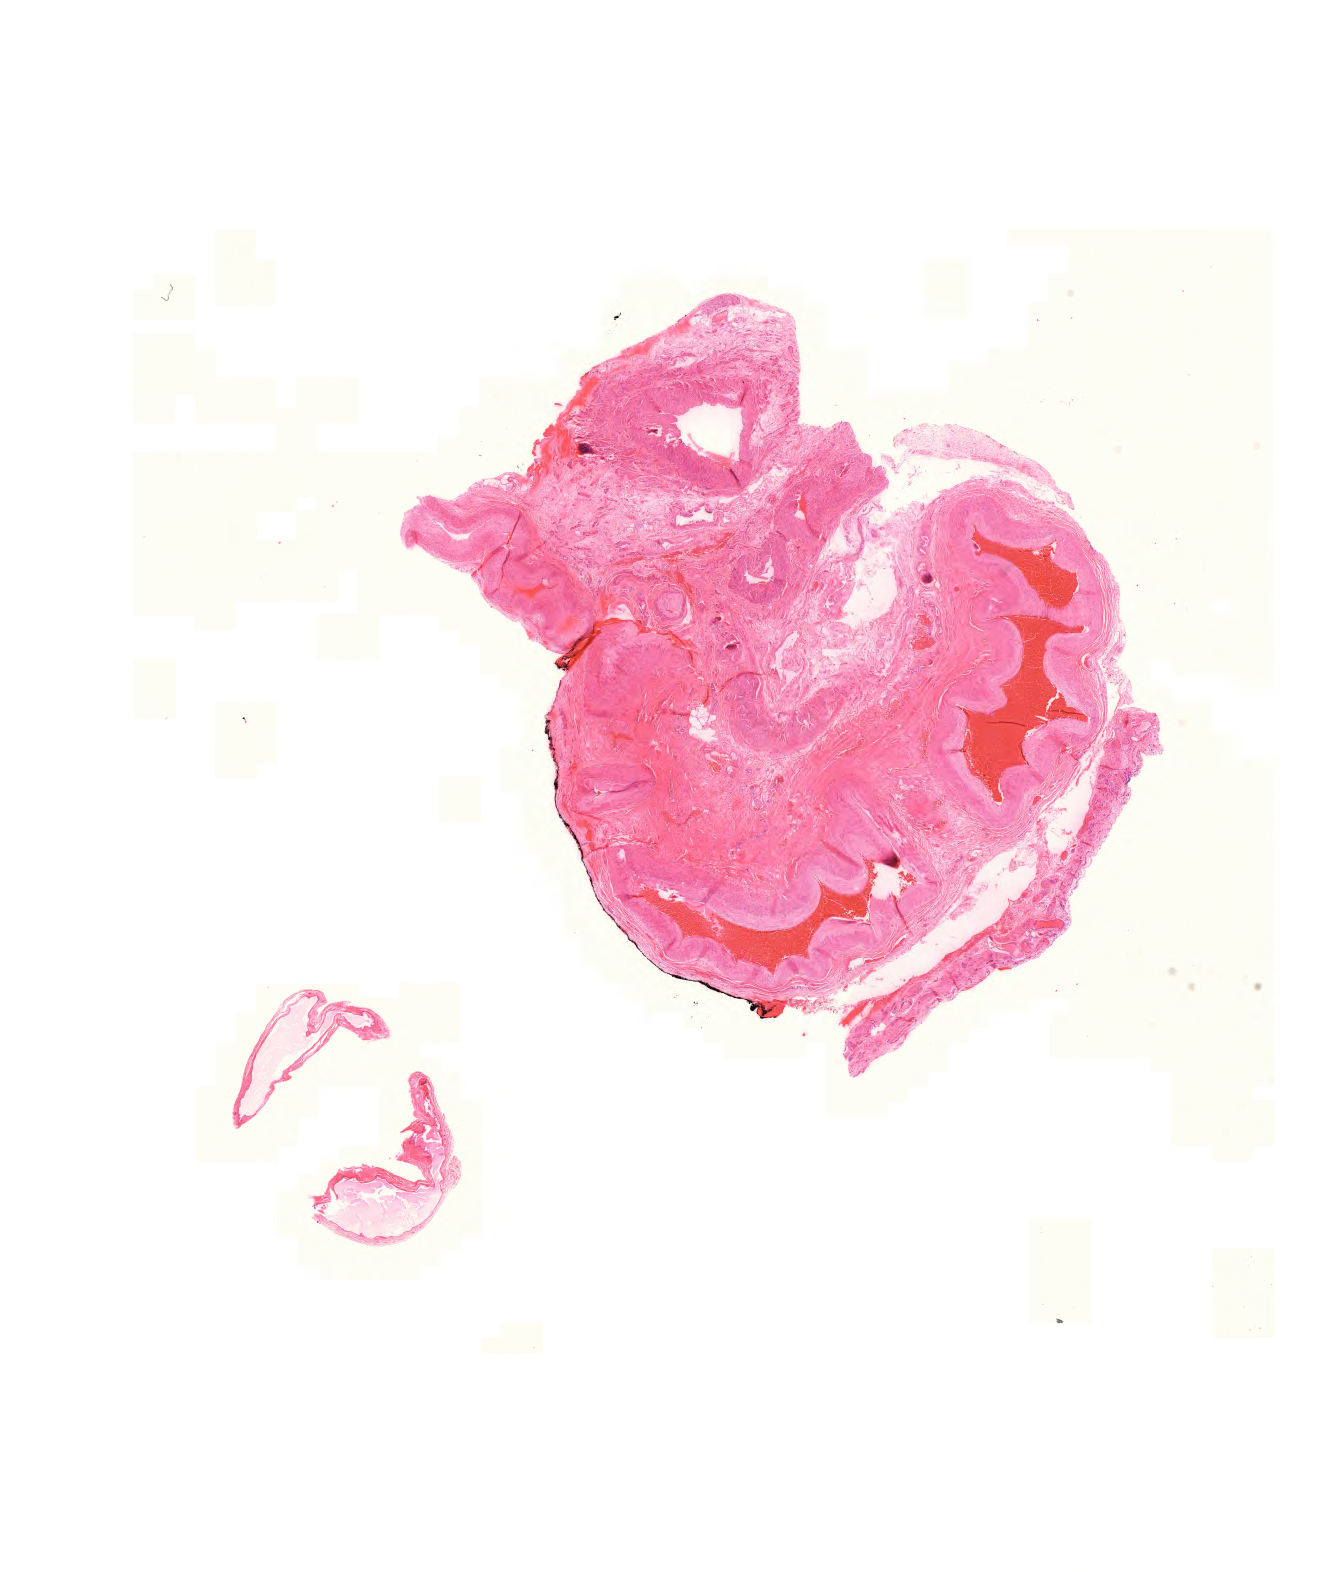
H&E whole-slide image — low-resolution overview of the scanned area, about 19.7 x 23.4 mm (slide scanned at 20x), FFPE section, colon, primary tumour sample. Male, age 82 years at initial diagnosis.
- diagnosis: Adenocarcinoma, NOS
- AJCC pathologic stage: IIA (7th edition)